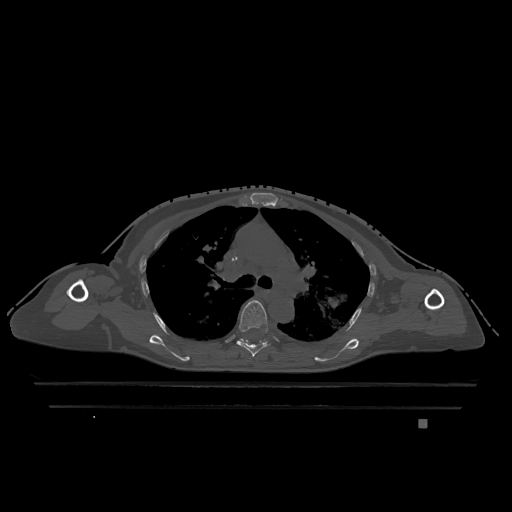
CT including the spine, one axial slice. Slice 829 of 1317 in the series (ordered by position). Bone window (W 1800 / L 400 HU). 0.5 mm slice thickness. 512 × 512 image matrix, field of view 500 × 500 mm. Female patient, age 74 years. From the clinical record (not read from this slice): primary cancer: lung; vertebrae with lytic lesions (as recorded): T1, T4, T5, T6, L4, L5.
Outlined on this slice (semi-automatic segmentation, software-assisted and operator-edited):
- T5 vertebra: box from (x=237, y=300) to (x=269, y=357) px
- T6 vertebra: (x=240, y=338)–(x=245, y=342)